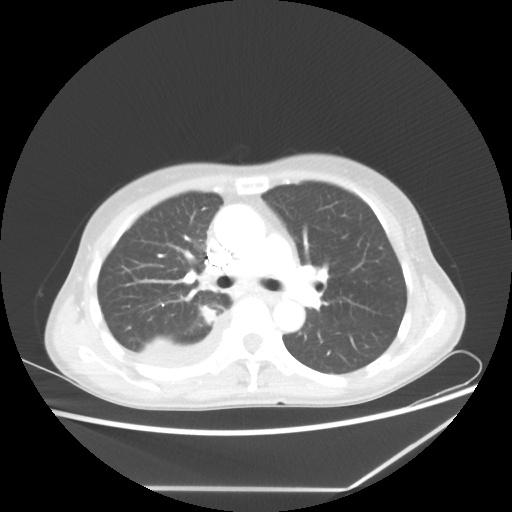
Chest CT, one axial slice; slice 37 of 60 in the series (ordered by position); reconstruction kernel STANDARD; 80 kVp; lung window (W 1500 / L -600 HU); 5 mm slice thickness; 512 × 512 image matrix, field of view 364 × 364 mm. Patient: female, 59 years. Case-level facts recorded for this patient, not image findings: clinical TNM (as recorded): T1c N1 M1.
Structures marked on this image (bounding box drawn by a radiologist):
- lung tumour (recorded histology: adenocarcinoma): box from (x=199, y=303) to (x=217, y=327) px